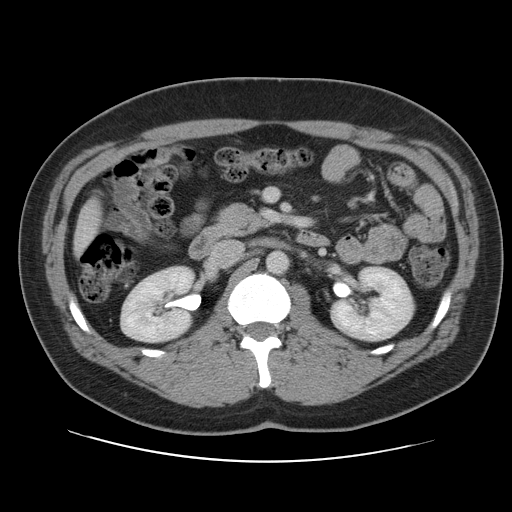
Contrast-enhanced abdominal CT, one axial slice; slice 46 of 109 in the series (ordered by position); intravenous contrast given; soft-tissue window (W 400 / L 40 HU); 5 mm slice thickness; 512 × 512 image matrix. Male patient, age 35 years. From the clinical record (not read from this slice): diagnosis: colorectal cancer liver metastases, imaged before liver resection; multiple liver metastases: yes; largest metastasis: 2.8 cm; chemotherapy before resection: yes.
Structures marked on this image (manually delineated by an expert):
- liver: bounding box <75,201,101,251> (left, top, right, bottom; pixels)
- planned liver remnant (the part of the liver to remain after resection): <75,202,101,251>